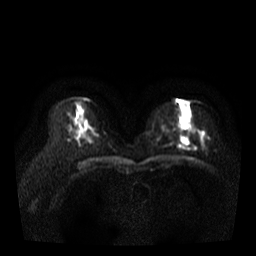
Breast MRI, one axial slice; position 17 of 35 along the scan axis; diffusion-weighted series; image 2 of 4 stored at this slice position (different b-values; order by instance number); 3 T; 5 mm slice thickness; 256 × 256 image matrix. Female patient.
Structures marked on this image (expert manual segmentation):
- tumour on diffusion-weighted imaging: bounding box [x1, y1, x2, y2] px = [181, 137, 189, 145]